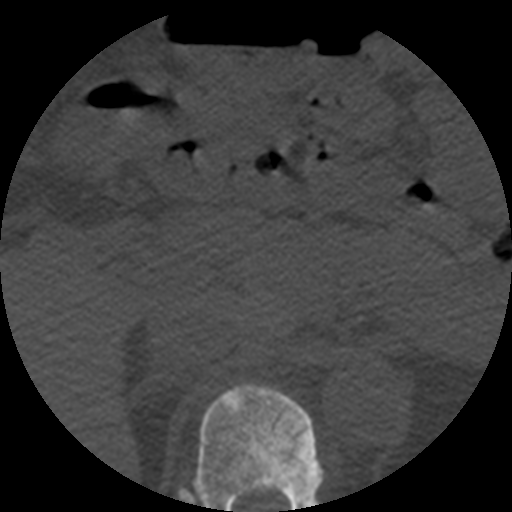
CT including the spine, one axial slice; slice 243 of 508 in the series (ordered by position); reconstruction kernel STANDARD; bone window (W 1800 / L 400 HU); 1.25 mm slice thickness; 512 × 512 image matrix, field of view 160 × 160 mm. Patient age 57 years. From the clinical record (not read from this slice): primary cancer: prostate.
Annotated regions visible in this slice (semi-automatic segmentation, software-assisted and operator-edited):
- T11 vertebra: bounding box (x1, y1, x2, y2) in pixels: (193, 383, 323, 512)